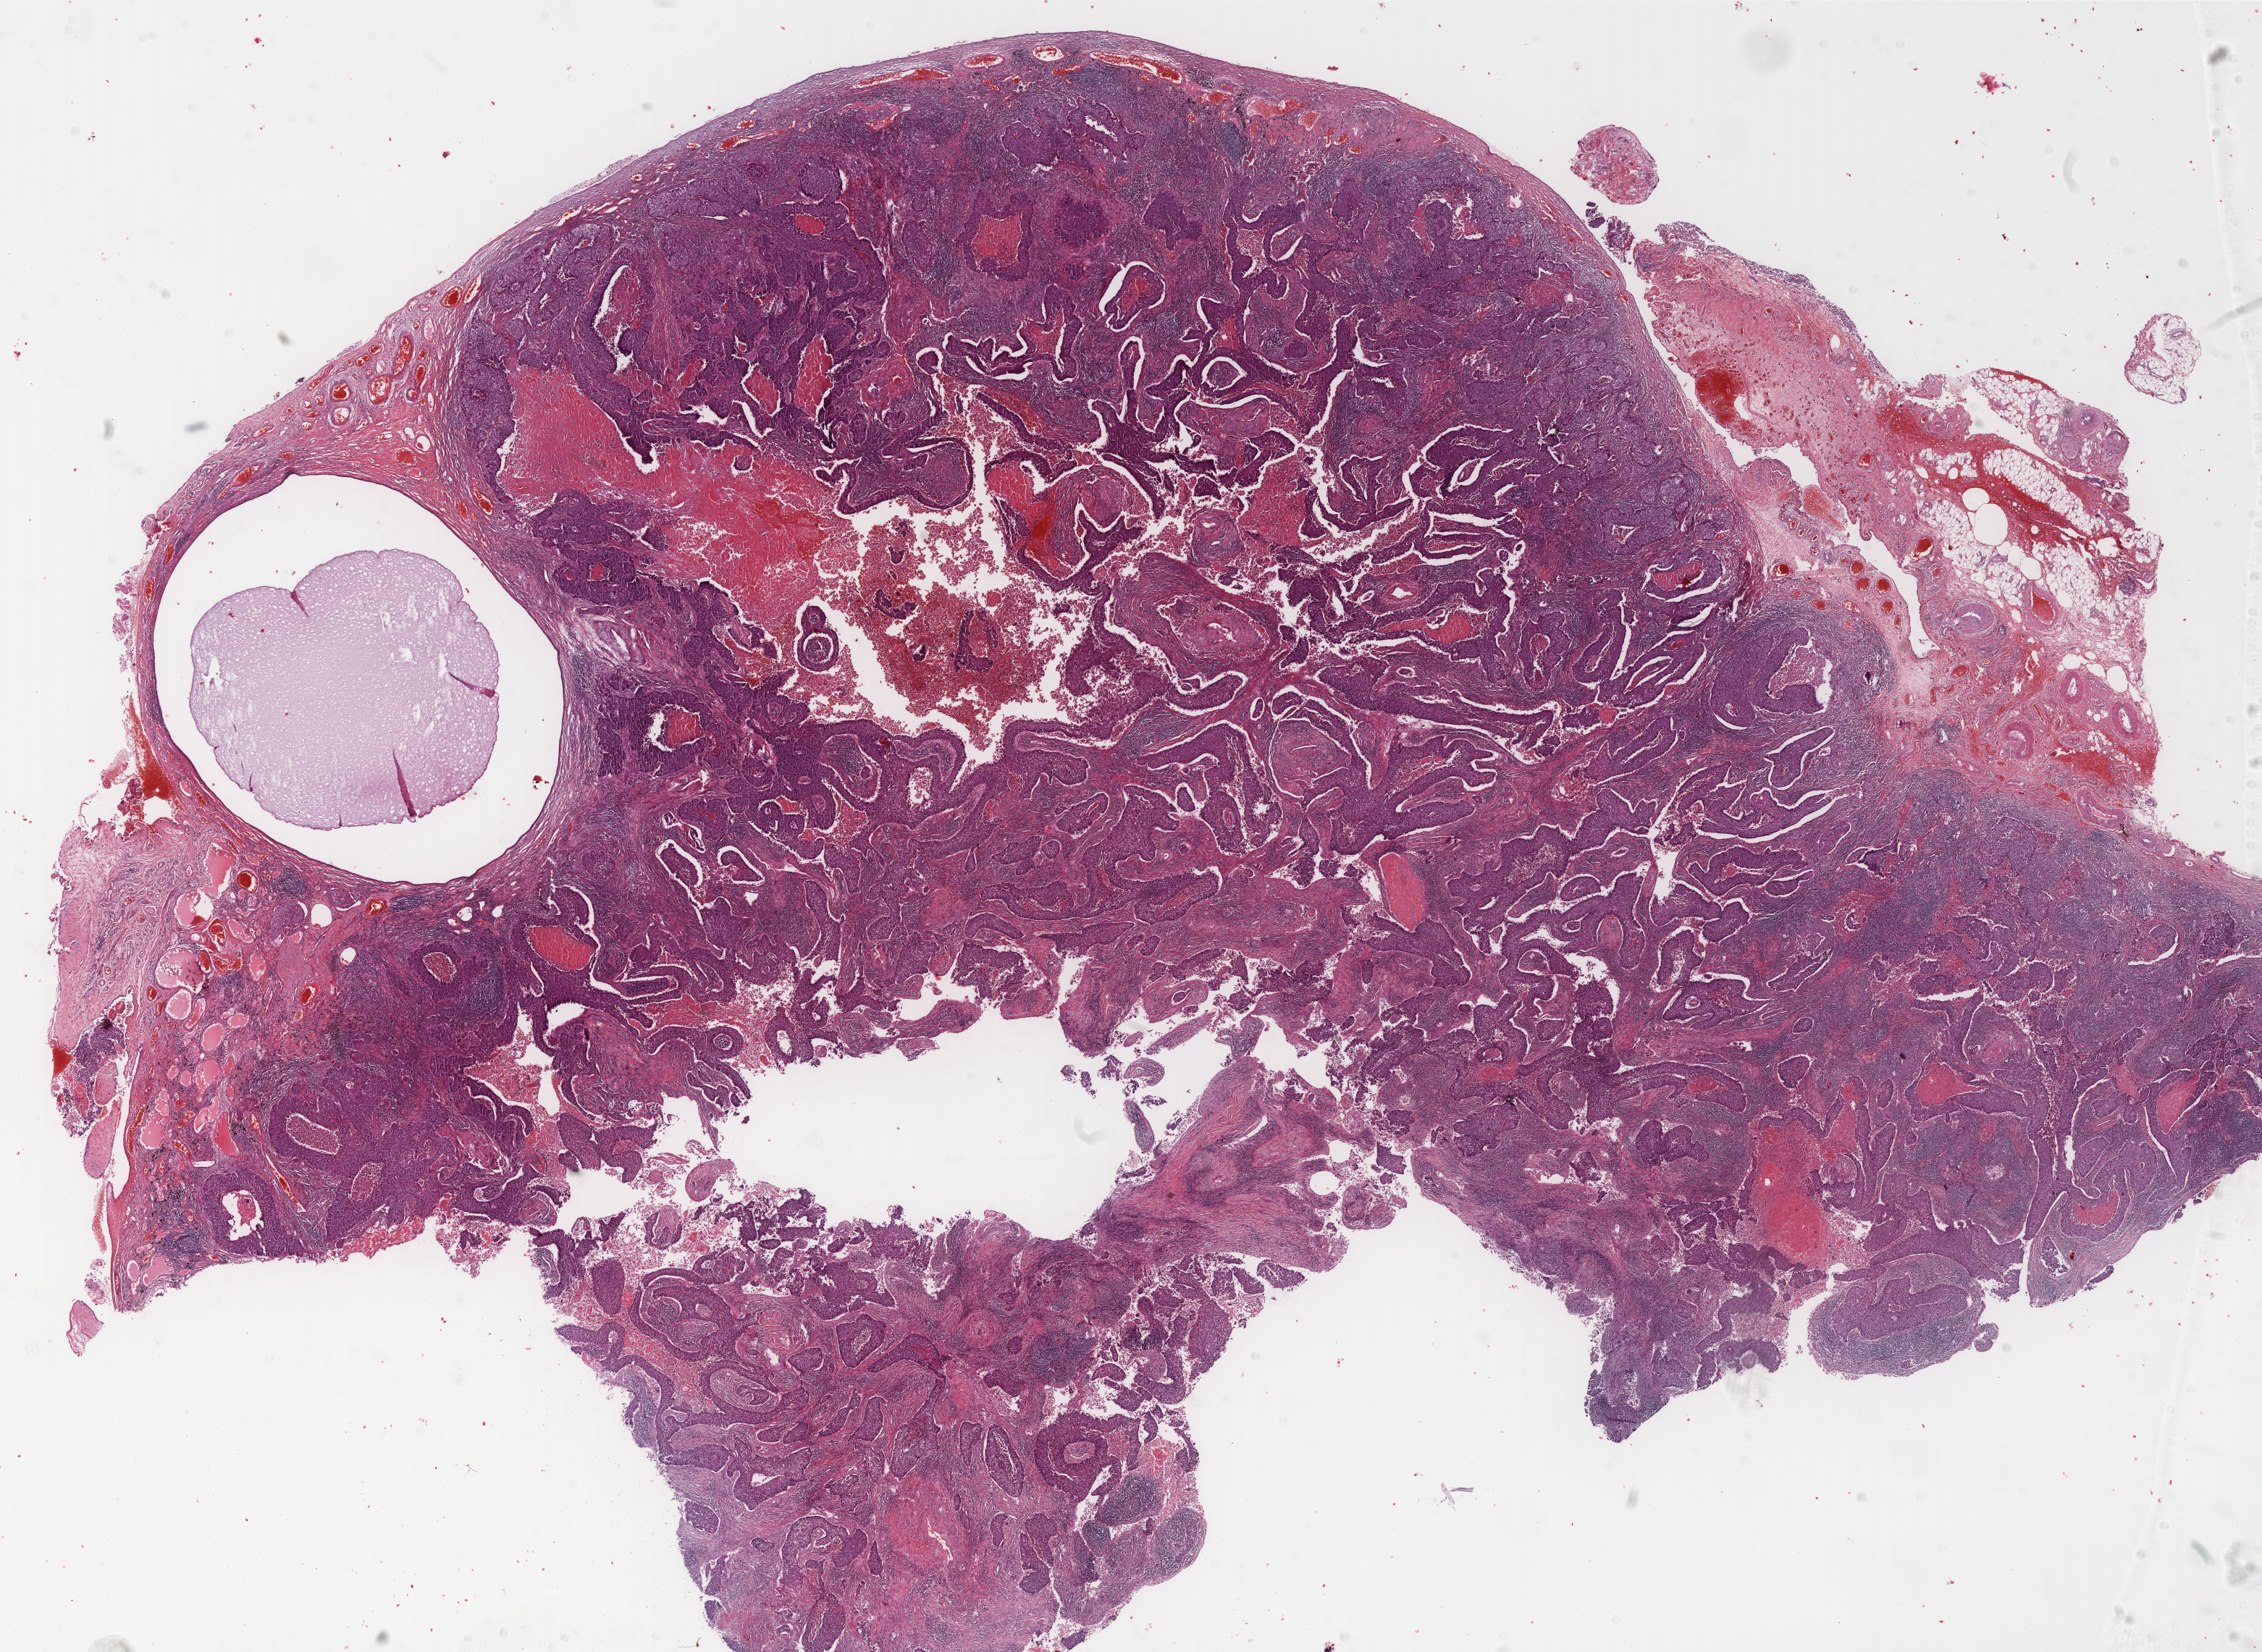
H&E whole-slide image — a low-resolution overview of the entire scanned area, about 25.2 x 18.4 mm (acquisition: 40x scan), formalin-fixed paraffin-embedded (FFPE) diagnostic section, primary tumour sample from the lung. Patient: male, age at initial diagnosis 59 years.
Laterality: right. AJCC pathologic stage: IIIA (6th edition). Histologic diagnosis: Basaloid squamous cell carcinoma (lower lobe, lung).